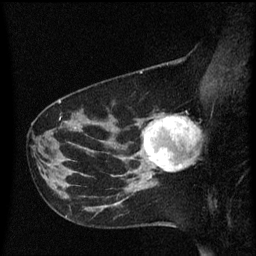
Breast MRI (dynamic contrast-enhanced), one sagittal slice. Slice 21 of 60 in the series (ordered by position). Dynamic contrast-enhanced series, image 2 of 3 at this slice position (ordered by acquisition). 1.5 T. TE 4.2 ms, TR 8.4 ms. 2 mm slice thickness. 256 × 256 image matrix, field of view 200 × 200 mm. Female patient, age 41 years. From the clinical record (not read from this slice): setting: breast cancer imaged before/during neoadjuvant chemotherapy; receptor status: triple-negative.
Outlined on this slice (semi-automatically segmented with operator editing):
- analysis volume of interest (the breast-tissue region the enhancement analysis was run in; not a lesion): box from (x=138, y=114) to (x=199, y=177) px
- tumour enhancement mask (voxels above the 70 % enhancement threshold inside the analysis volume of interest): (x=144, y=118)–(x=196, y=171)